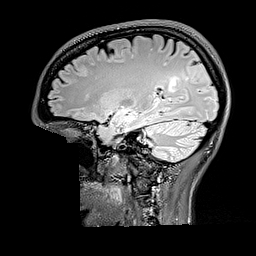
Brain MRI from a brain-tumour surgery series, one sagittal slice; slice 110 of 176 in the series (ordered by position); T2 FLAIR; 1 mm slice thickness; 256 × 256 image matrix, field of view 256 × 256 mm. From the clinical record (not read from this slice): histopathology: Oligodendroglioma; WHO grade: 2; IDH mutation: yes.
Annotated regions visible in this slice (expert manual segmentation):
- tumour: bounding box <168,76,181,94> (left, top, right, bottom; pixels)